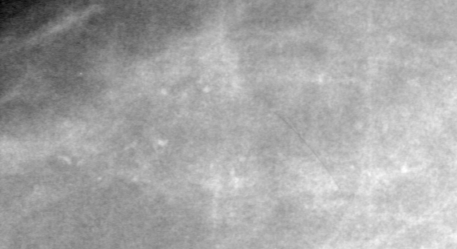
Crop from a digitized film mammogram around one marked abnormality, left breast, CC view.
Marked abnormality: calcifications, morphology pleomorphic, distribution clustered; BI-RADS assessment category 4; pathology result (as recorded, not read from the image): malignant.